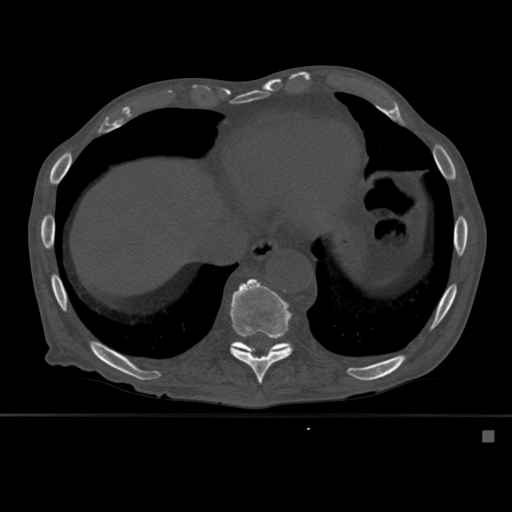
CT including the spine, one axial slice. Slice 311 of 527 in the series (ordered by position). Bone window (W 1800 / L 400 HU). 1.5 mm slice thickness. 512 × 512 image matrix, field of view 373 × 373 mm. Male patient, age 78 years. From the clinical record (not read from this slice): primary cancer: prostate.
Outlined on this slice (semi-automatic segmentation, software-assisted and operator-edited):
- T10 vertebra: bounding box (x1, y1, x2, y2) in pixels: (229, 278, 292, 384)
- T11 vertebra: (233, 338, 293, 355)